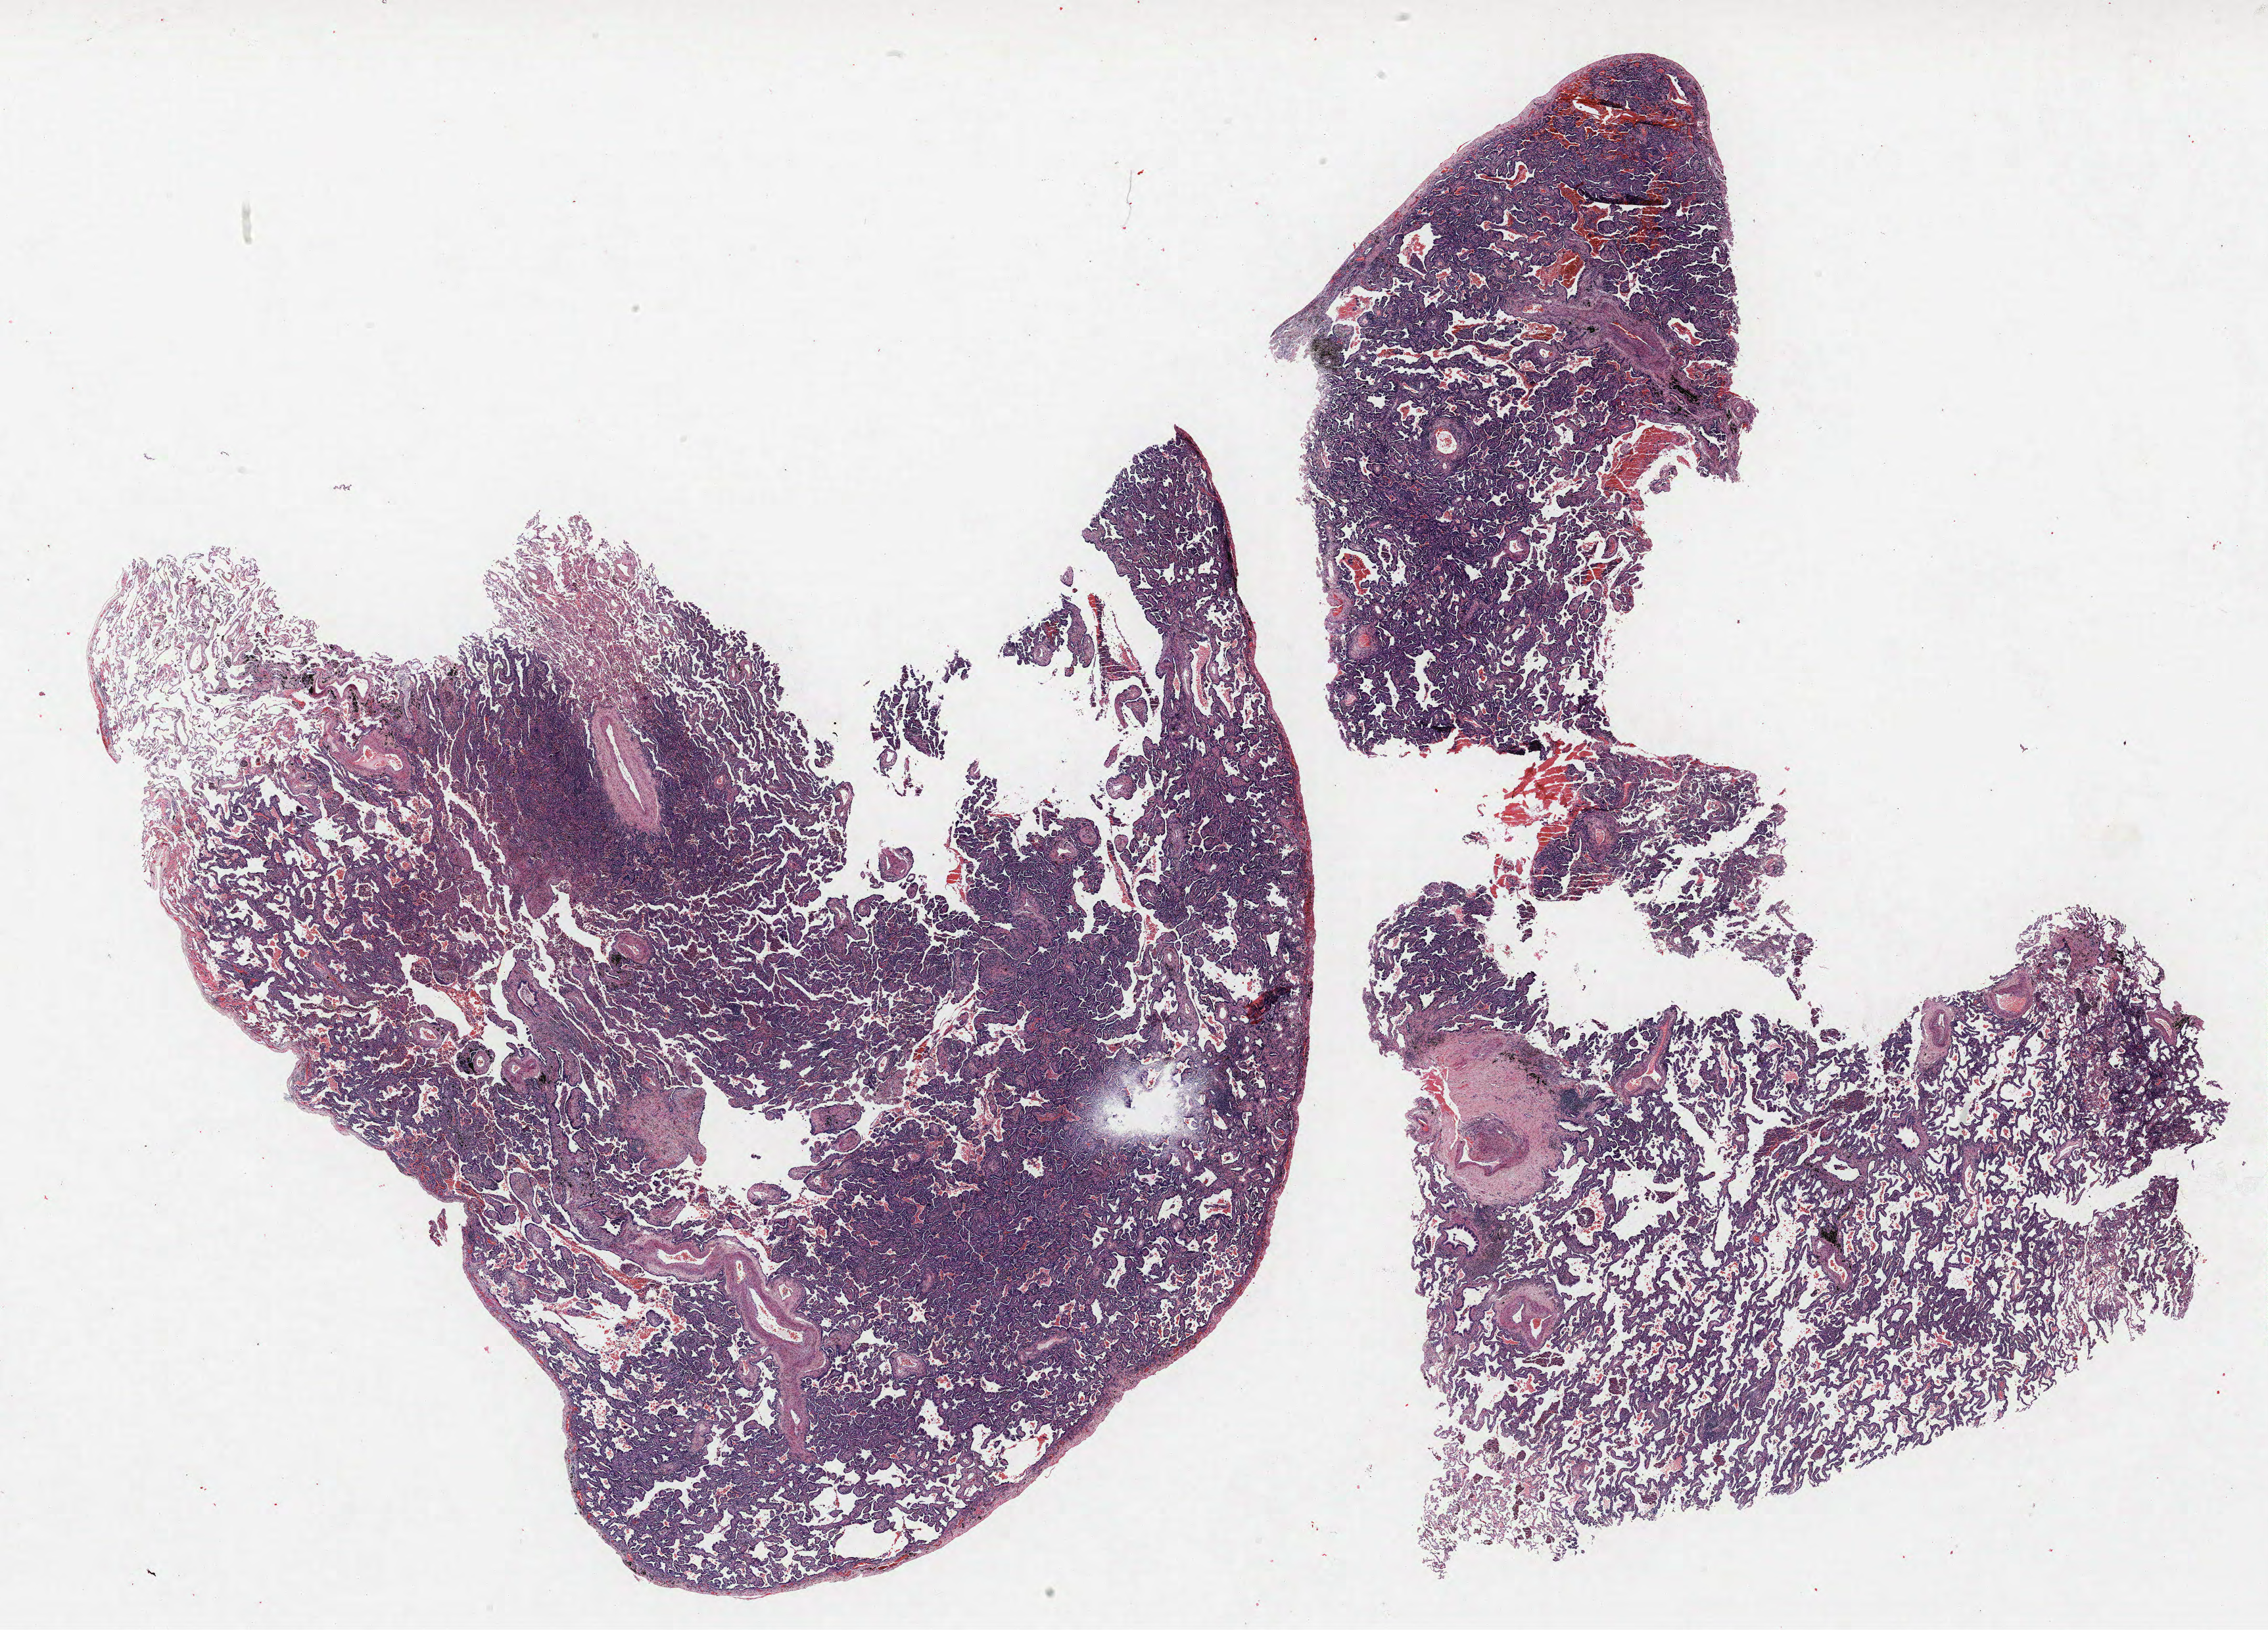
Whole-slide histology image, H&E-stained — shown as a low-resolution overview of the whole scanned area (about 27.6 x 19.8 mm); FFPE section; lung. Female, age 64 at enrolment. Current smoker at enrolment. Grade: well differentiated (G1).
* participant's lung-cancer diagnosis: Bronchiolo-alveolar carcinoma, non-mucinous
* tumour size (pathology): 20 mm
* stage (AJCC 6th edition): IA
* primary tumour location (clinical record): right lower lobe